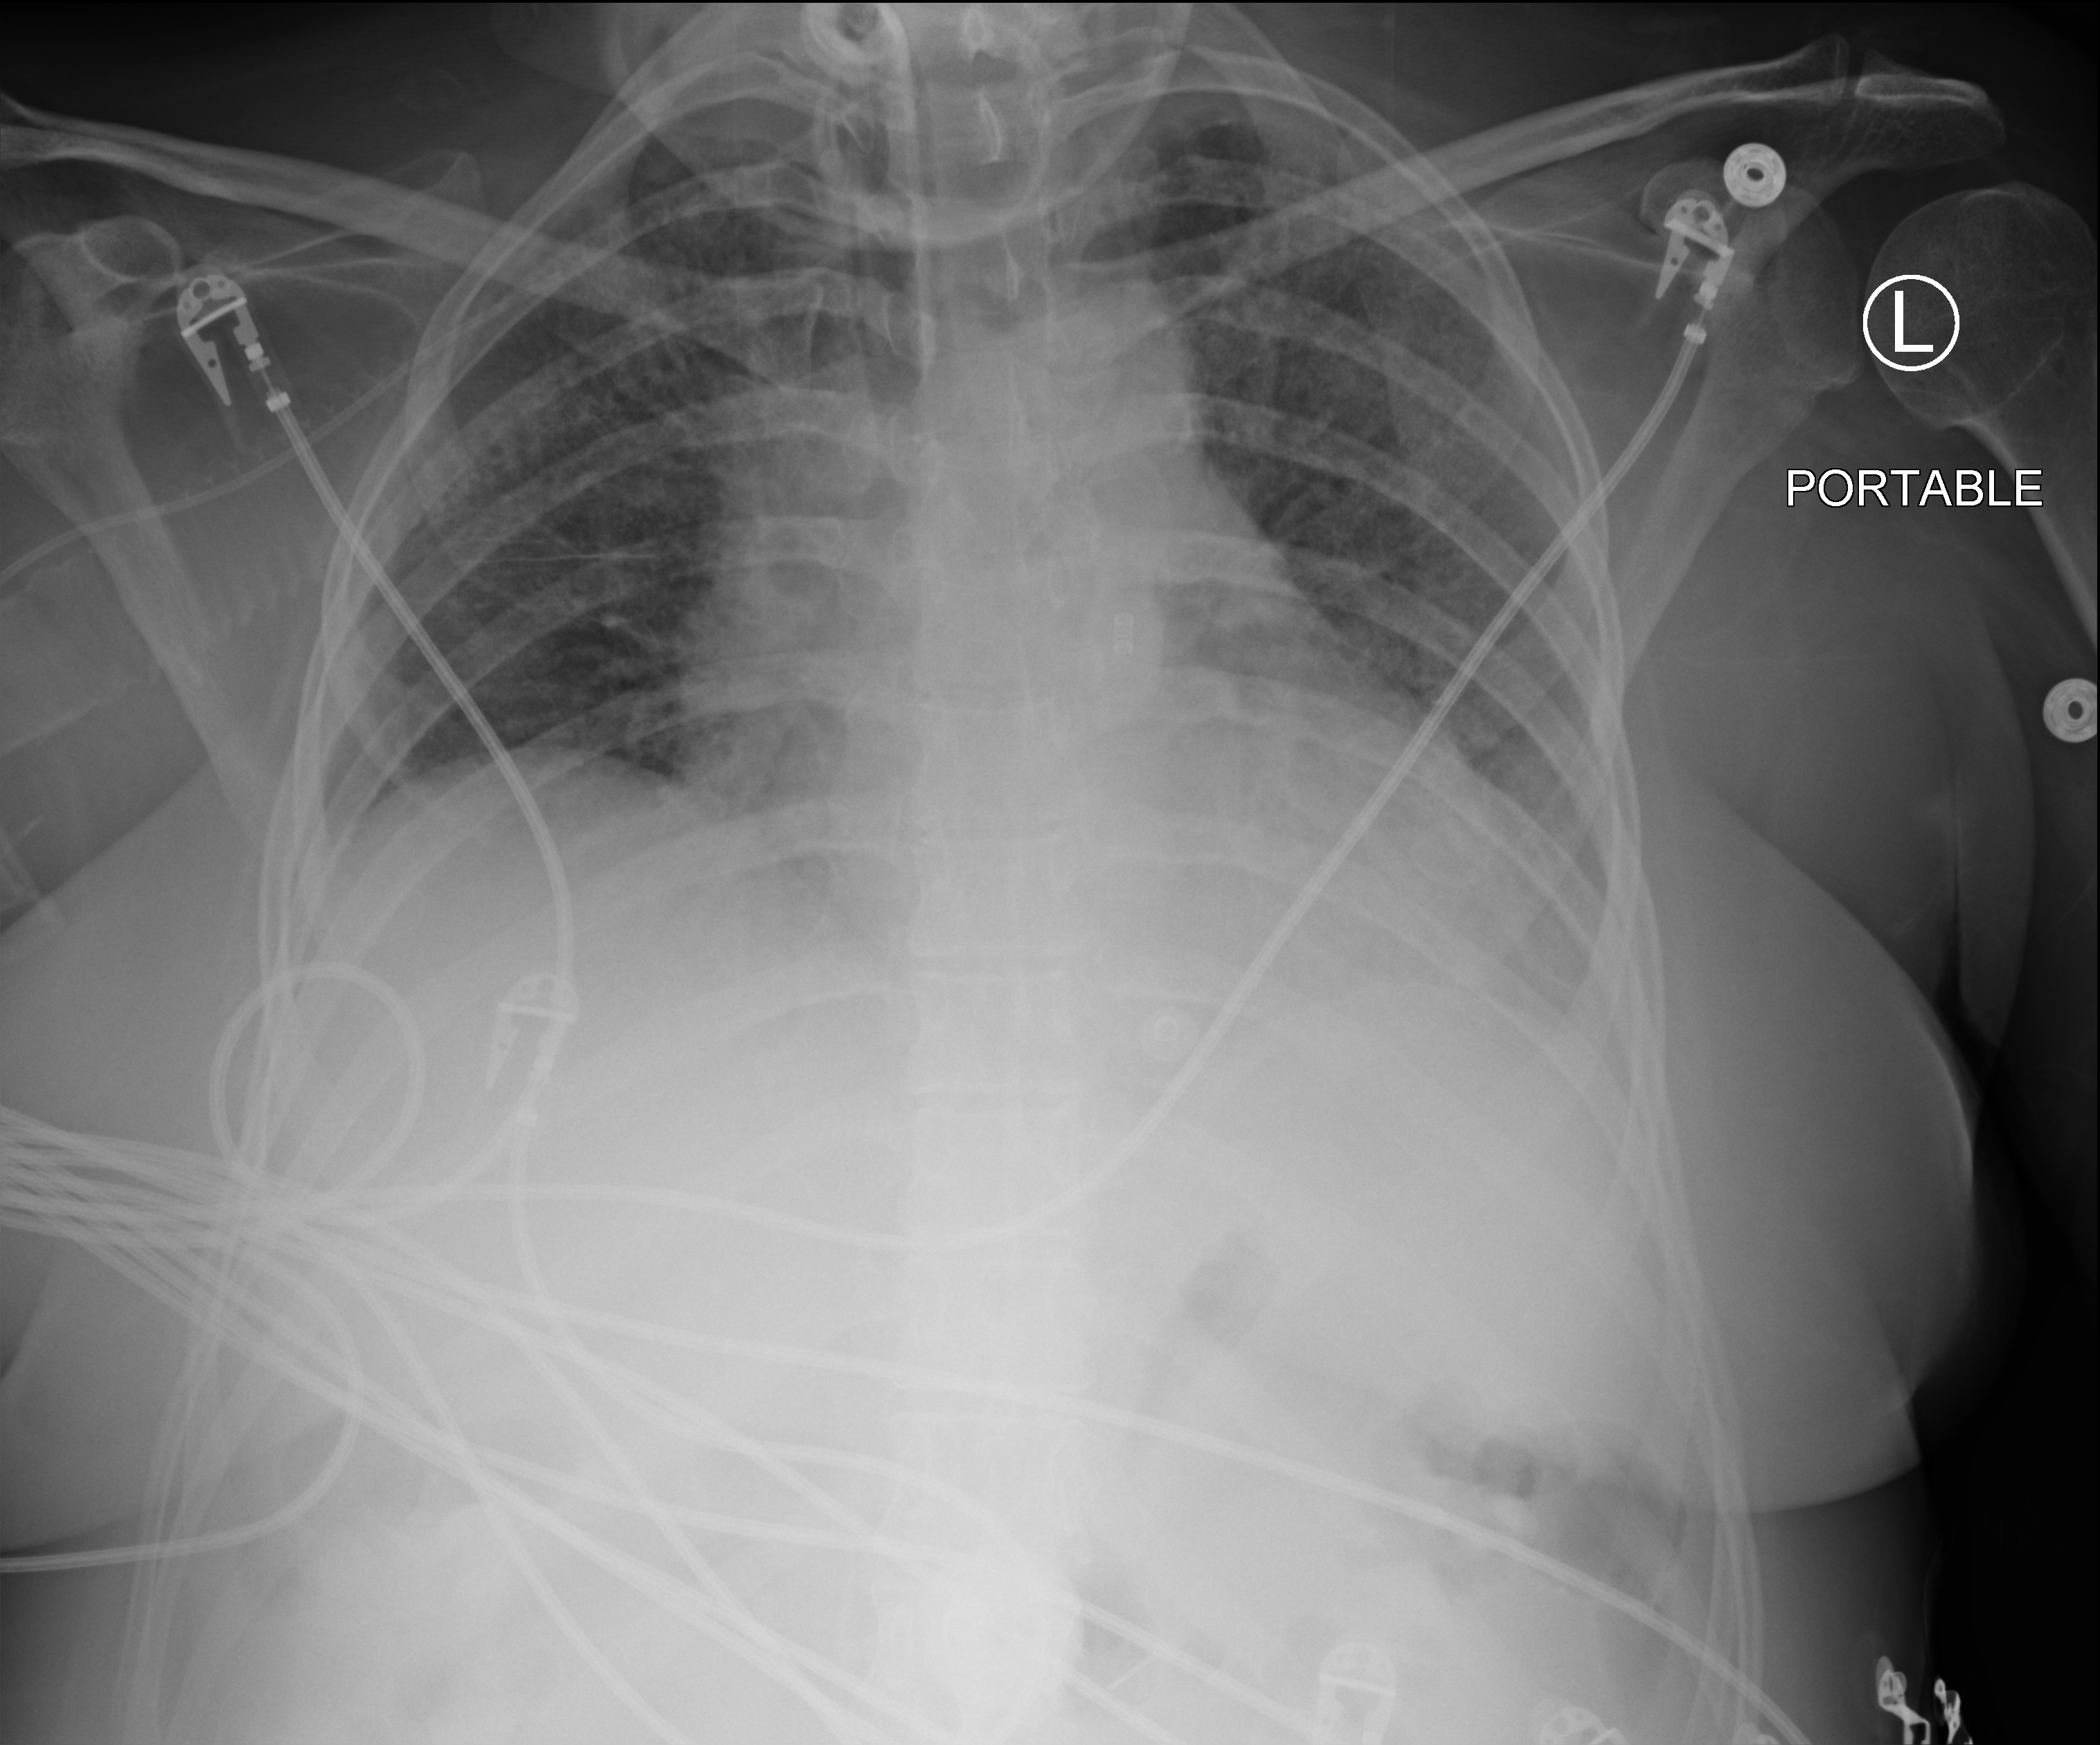
Bedside chest radiograph (computed radiography). Patient hospitalised with COVID-19; female, aged 18–59 years.
From the hospital-stay record, not from the radiograph (when in the stay this image was taken is not recorded):
- admitted to intensive care during this hospital stay: yes
- mechanically ventilated during this hospital stay: yes
- COPD (admission record): no